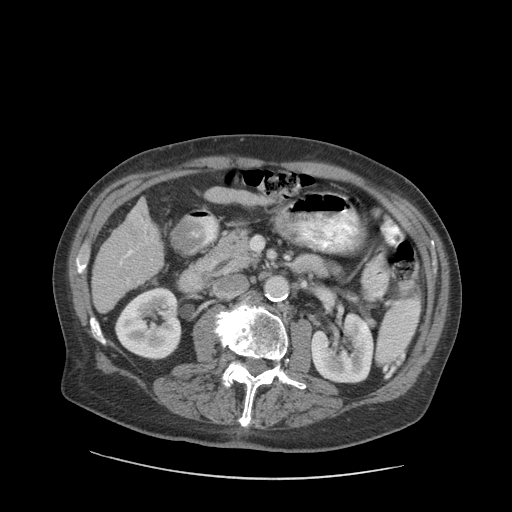
Contrast-enhanced abdominal CT (liver protocol), one axial slice; 140 kVp; soft-tissue window (W 400 / L 40 HU); 2.5 mm slice thickness; 512 × 512 image matrix, field of view 420 × 420 mm. From the clinical record (not read from this slice): diagnosis: hepatocellular carcinoma (patient treated with transarterial chemoembolisation; whether this scan precedes or follows treatment is not stated here); TNM stage (as recorded): Stage-I; Child-Pugh class: A; tumour differentiation: moderately differentiated; tumour size: 4.6 cm.
Structures marked on this image (semi-automatically segmented with operator editing):
- liver parenchyma outside the tumour (the mass and vessels are separate outlines, so this box may not span the whole liver): bounding box <92,200,162,312> (left, top, right, bottom; pixels)
- mass: <122,213,156,244>
- liver vessels: <119,211,138,284>